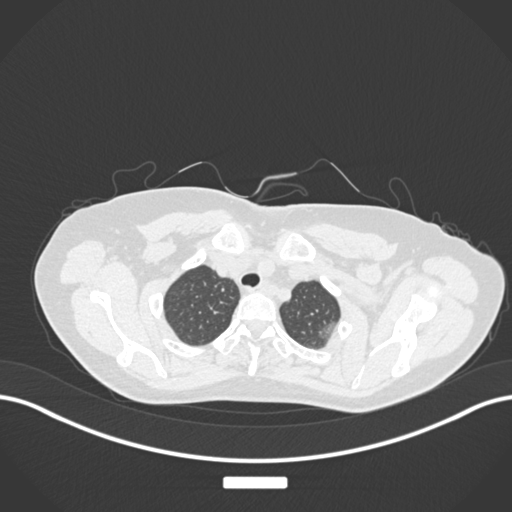
Chest CT, one axial slice; position 153 of 181 along the scan axis; reconstruction kernel B30f; 120 kVp; lung window (W 1500 / L -600 HU); 1 mm slice thickness; 512 × 512 image matrix. Female patient, age 58 years. From the clinical record (not read from this slice): clinical TNM (as recorded): T1c N0 M0.
Outlined on this slice (rectangle marked by the reading radiologist):
- lung tumour (recorded histology: adenocarcinoma): bounding box <314,314,341,344> (left, top, right, bottom; pixels)